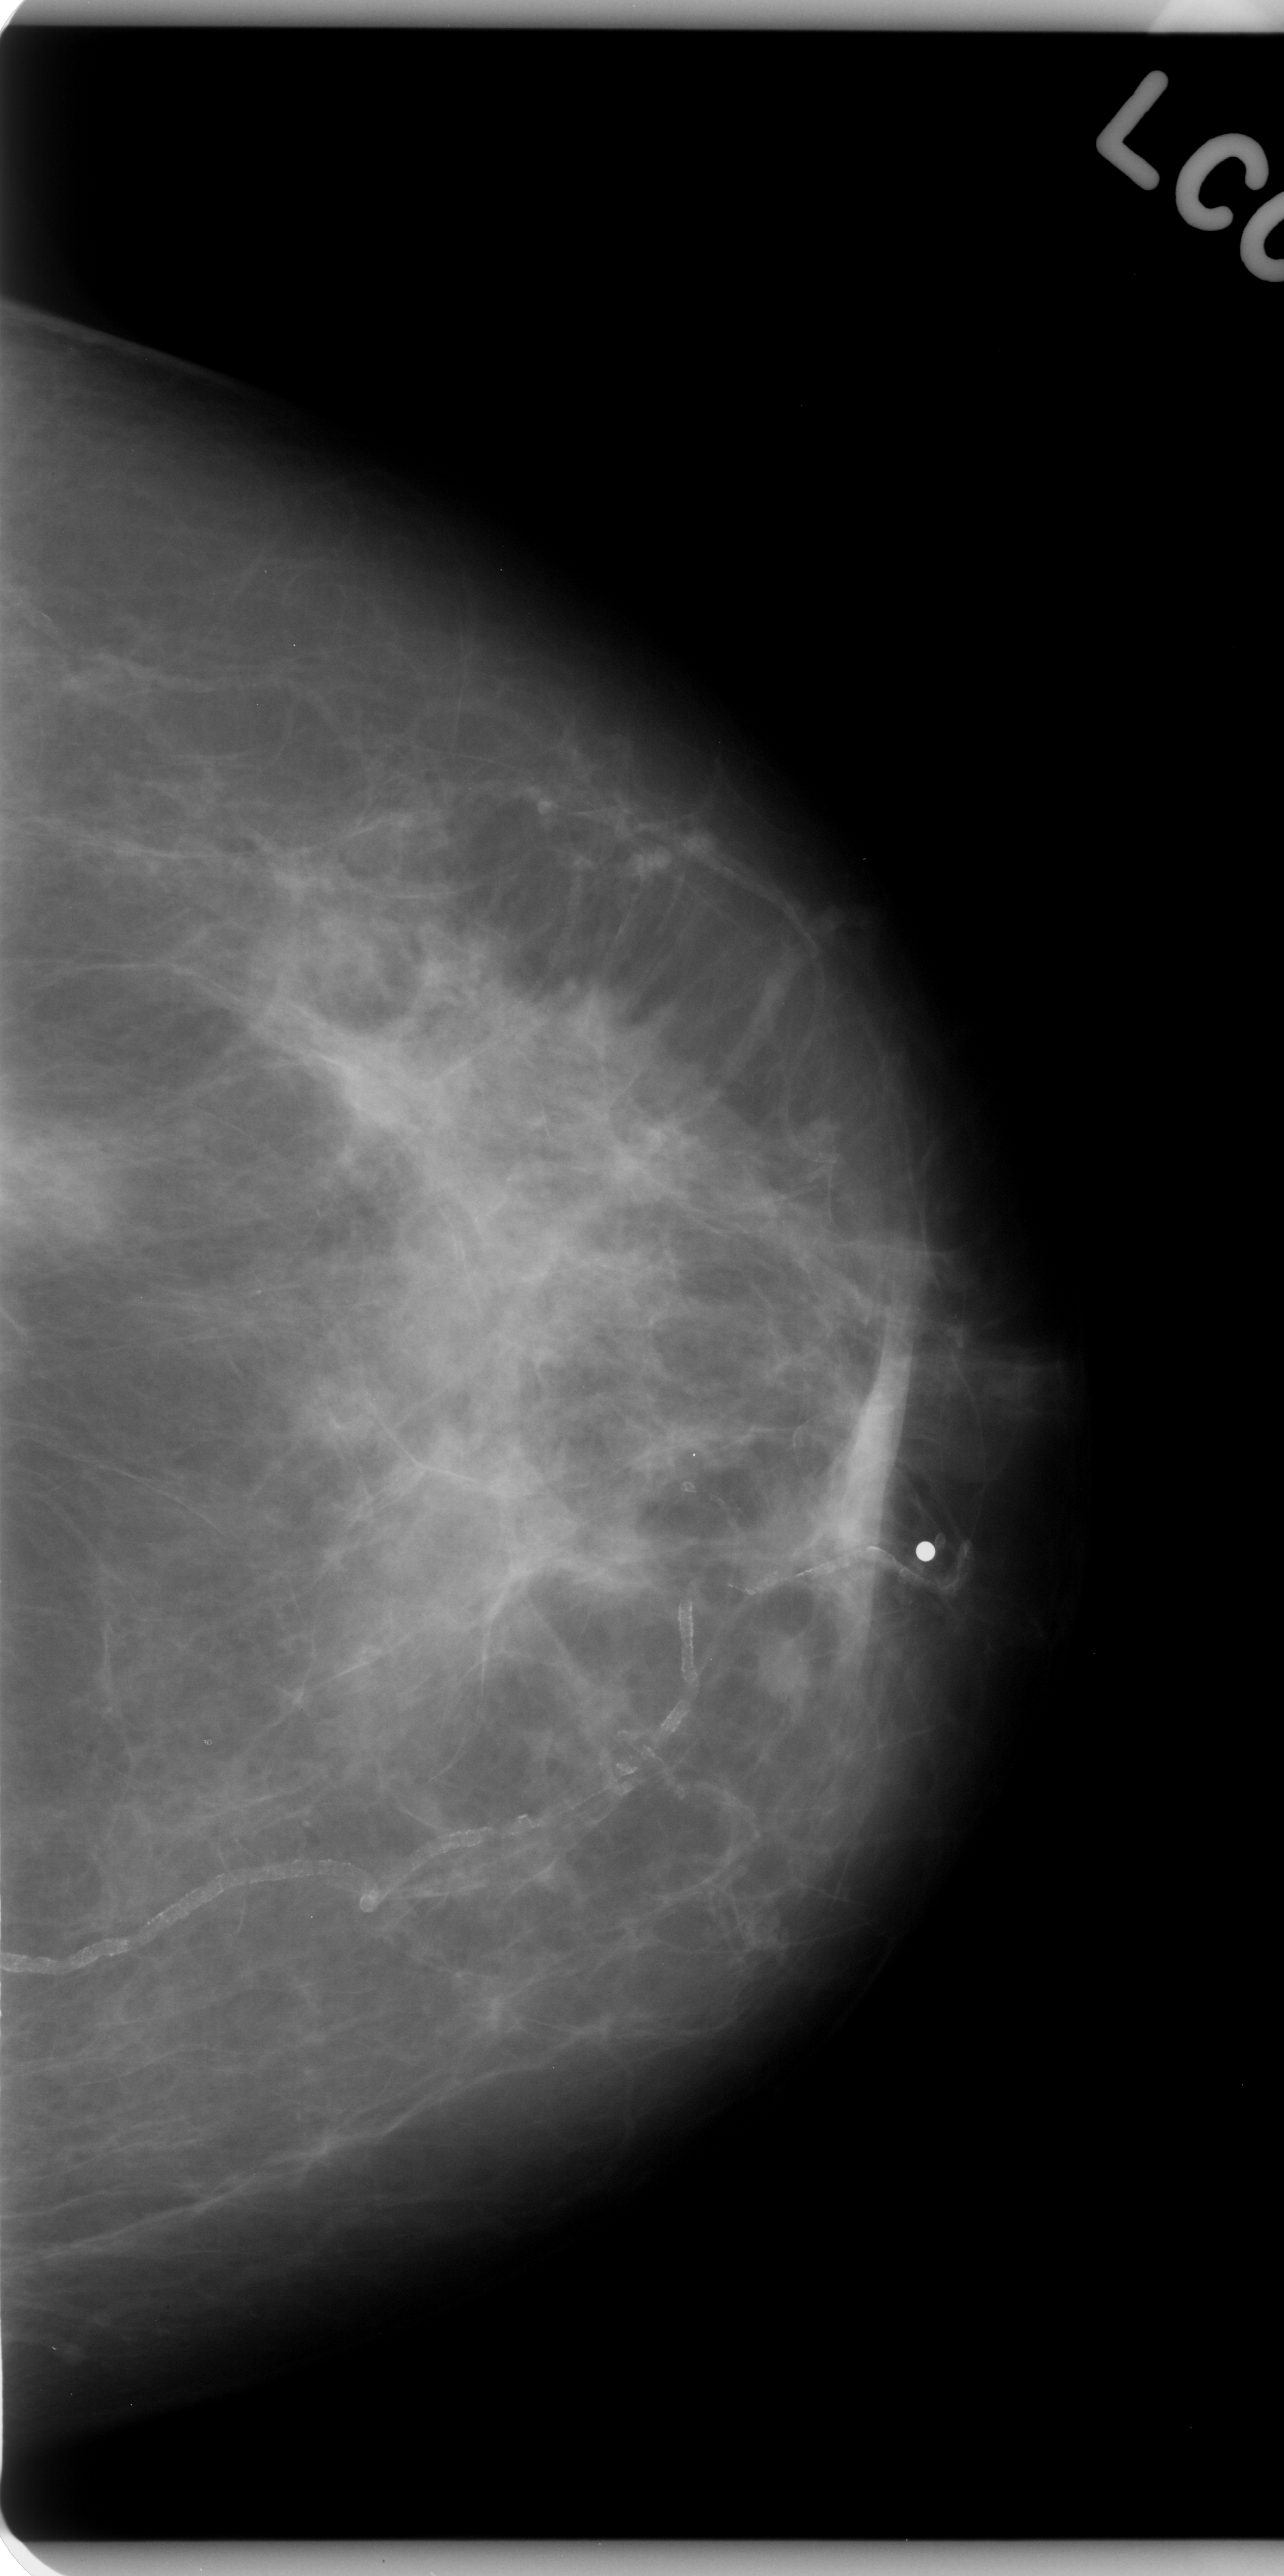
Scanned film-screen mammogram, left breast, craniocaudal (CC) view, breast composition: scattered fibroglandular densities (BI-RADS density category 2 of 4).
Abnormality record for this image: Finding 1 of 2: mass, shape oval, margins ill defined; BI-RADS assessment category 4; subtlety rating 4 on a 1 (subtle) to 5 (obvious) scale; pathology result (as recorded, not read from the image): malignant. Finding 2 of 2: mass, shape irregular, margins ill defined; BI-RADS assessment category 5; pathology result (as recorded, not read from the image): malignant.